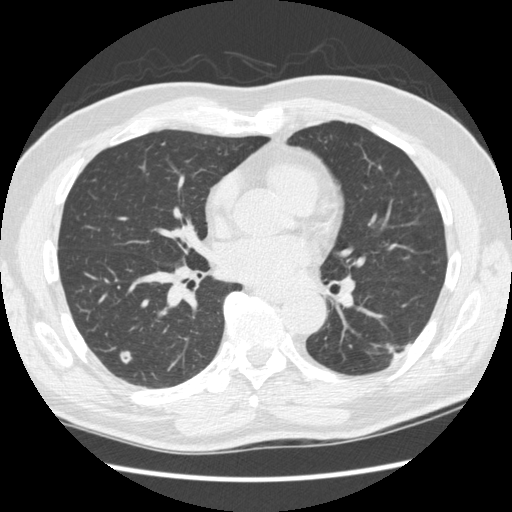
Axial slice from a low-dose chest CT screening exam. Baseline screening round. Lung window (W 1500 / L -600 HU). 1.25 mm slice thickness. Standard (soft-tissue) reconstruction kernel (STANDARD). Slice 132 of 267 in the series. 512 × 512 image matrix. Male participant, aged 74 years at enrolment. Former smoker at enrolment.
Expert reader's lesion annotation, bounding box (x1, y1, x2, y2) in pixels: (376, 324, 418, 376). The screening reader recorded 3 non-calcified nodules or masses ≥4 mm on this exam (right upper lobe, right lower lobe, left upper lobe); which of them this box marks is not recorded.